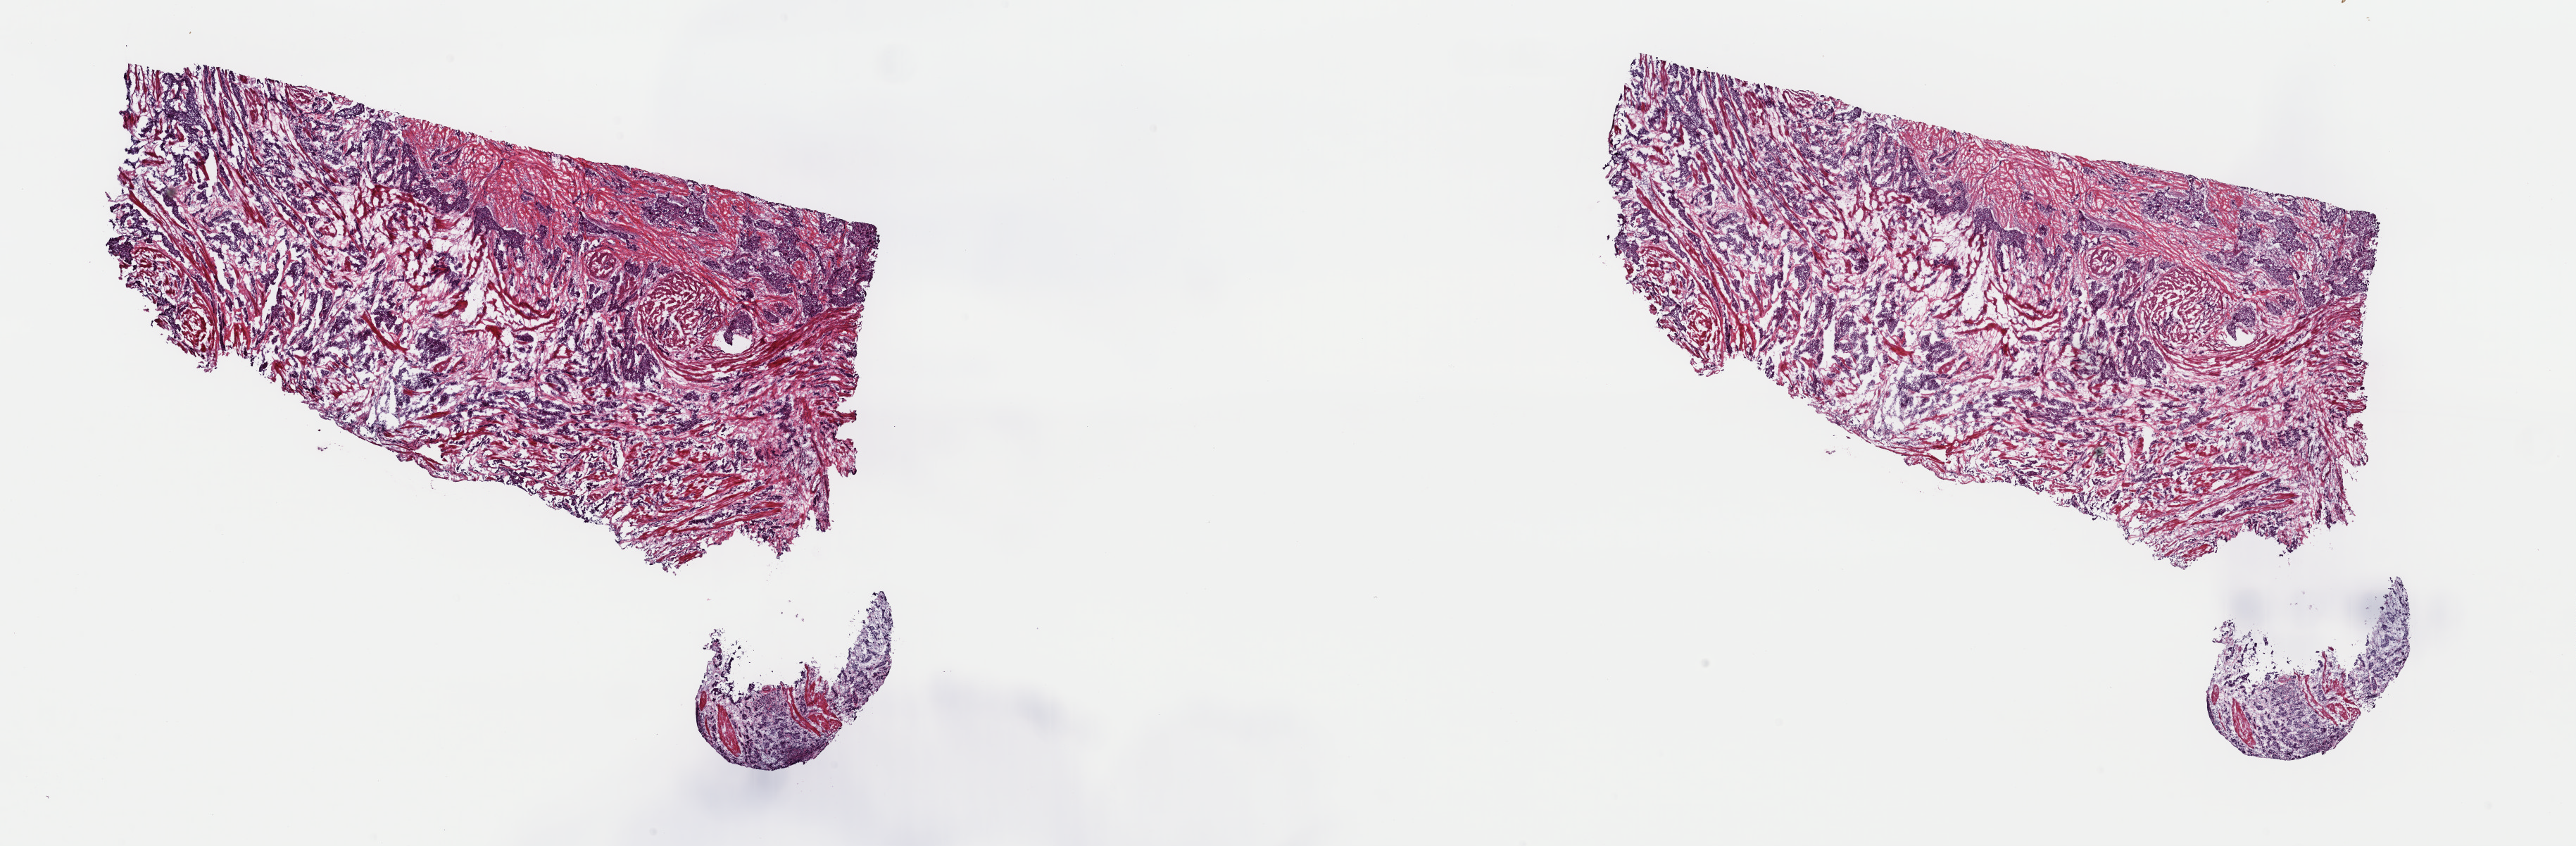
Digitized Hematoxylin and eosin (H&E) stained tissue section (whole slide) — shown as a low-resolution overview of the whole scanned area (about 28.9 x 9.5 mm, from a 40x scan); frozen section from the top of the tissue portion; primary tumour sample from the esophagus. Male, age 61 years at initial diagnosis. Slide review estimates, as recorded: tumour cells 65%, tumour nuclei 100%.
Pathologic diagnosis: Squamous cell carcinoma, NOS (lower third of esophagus).